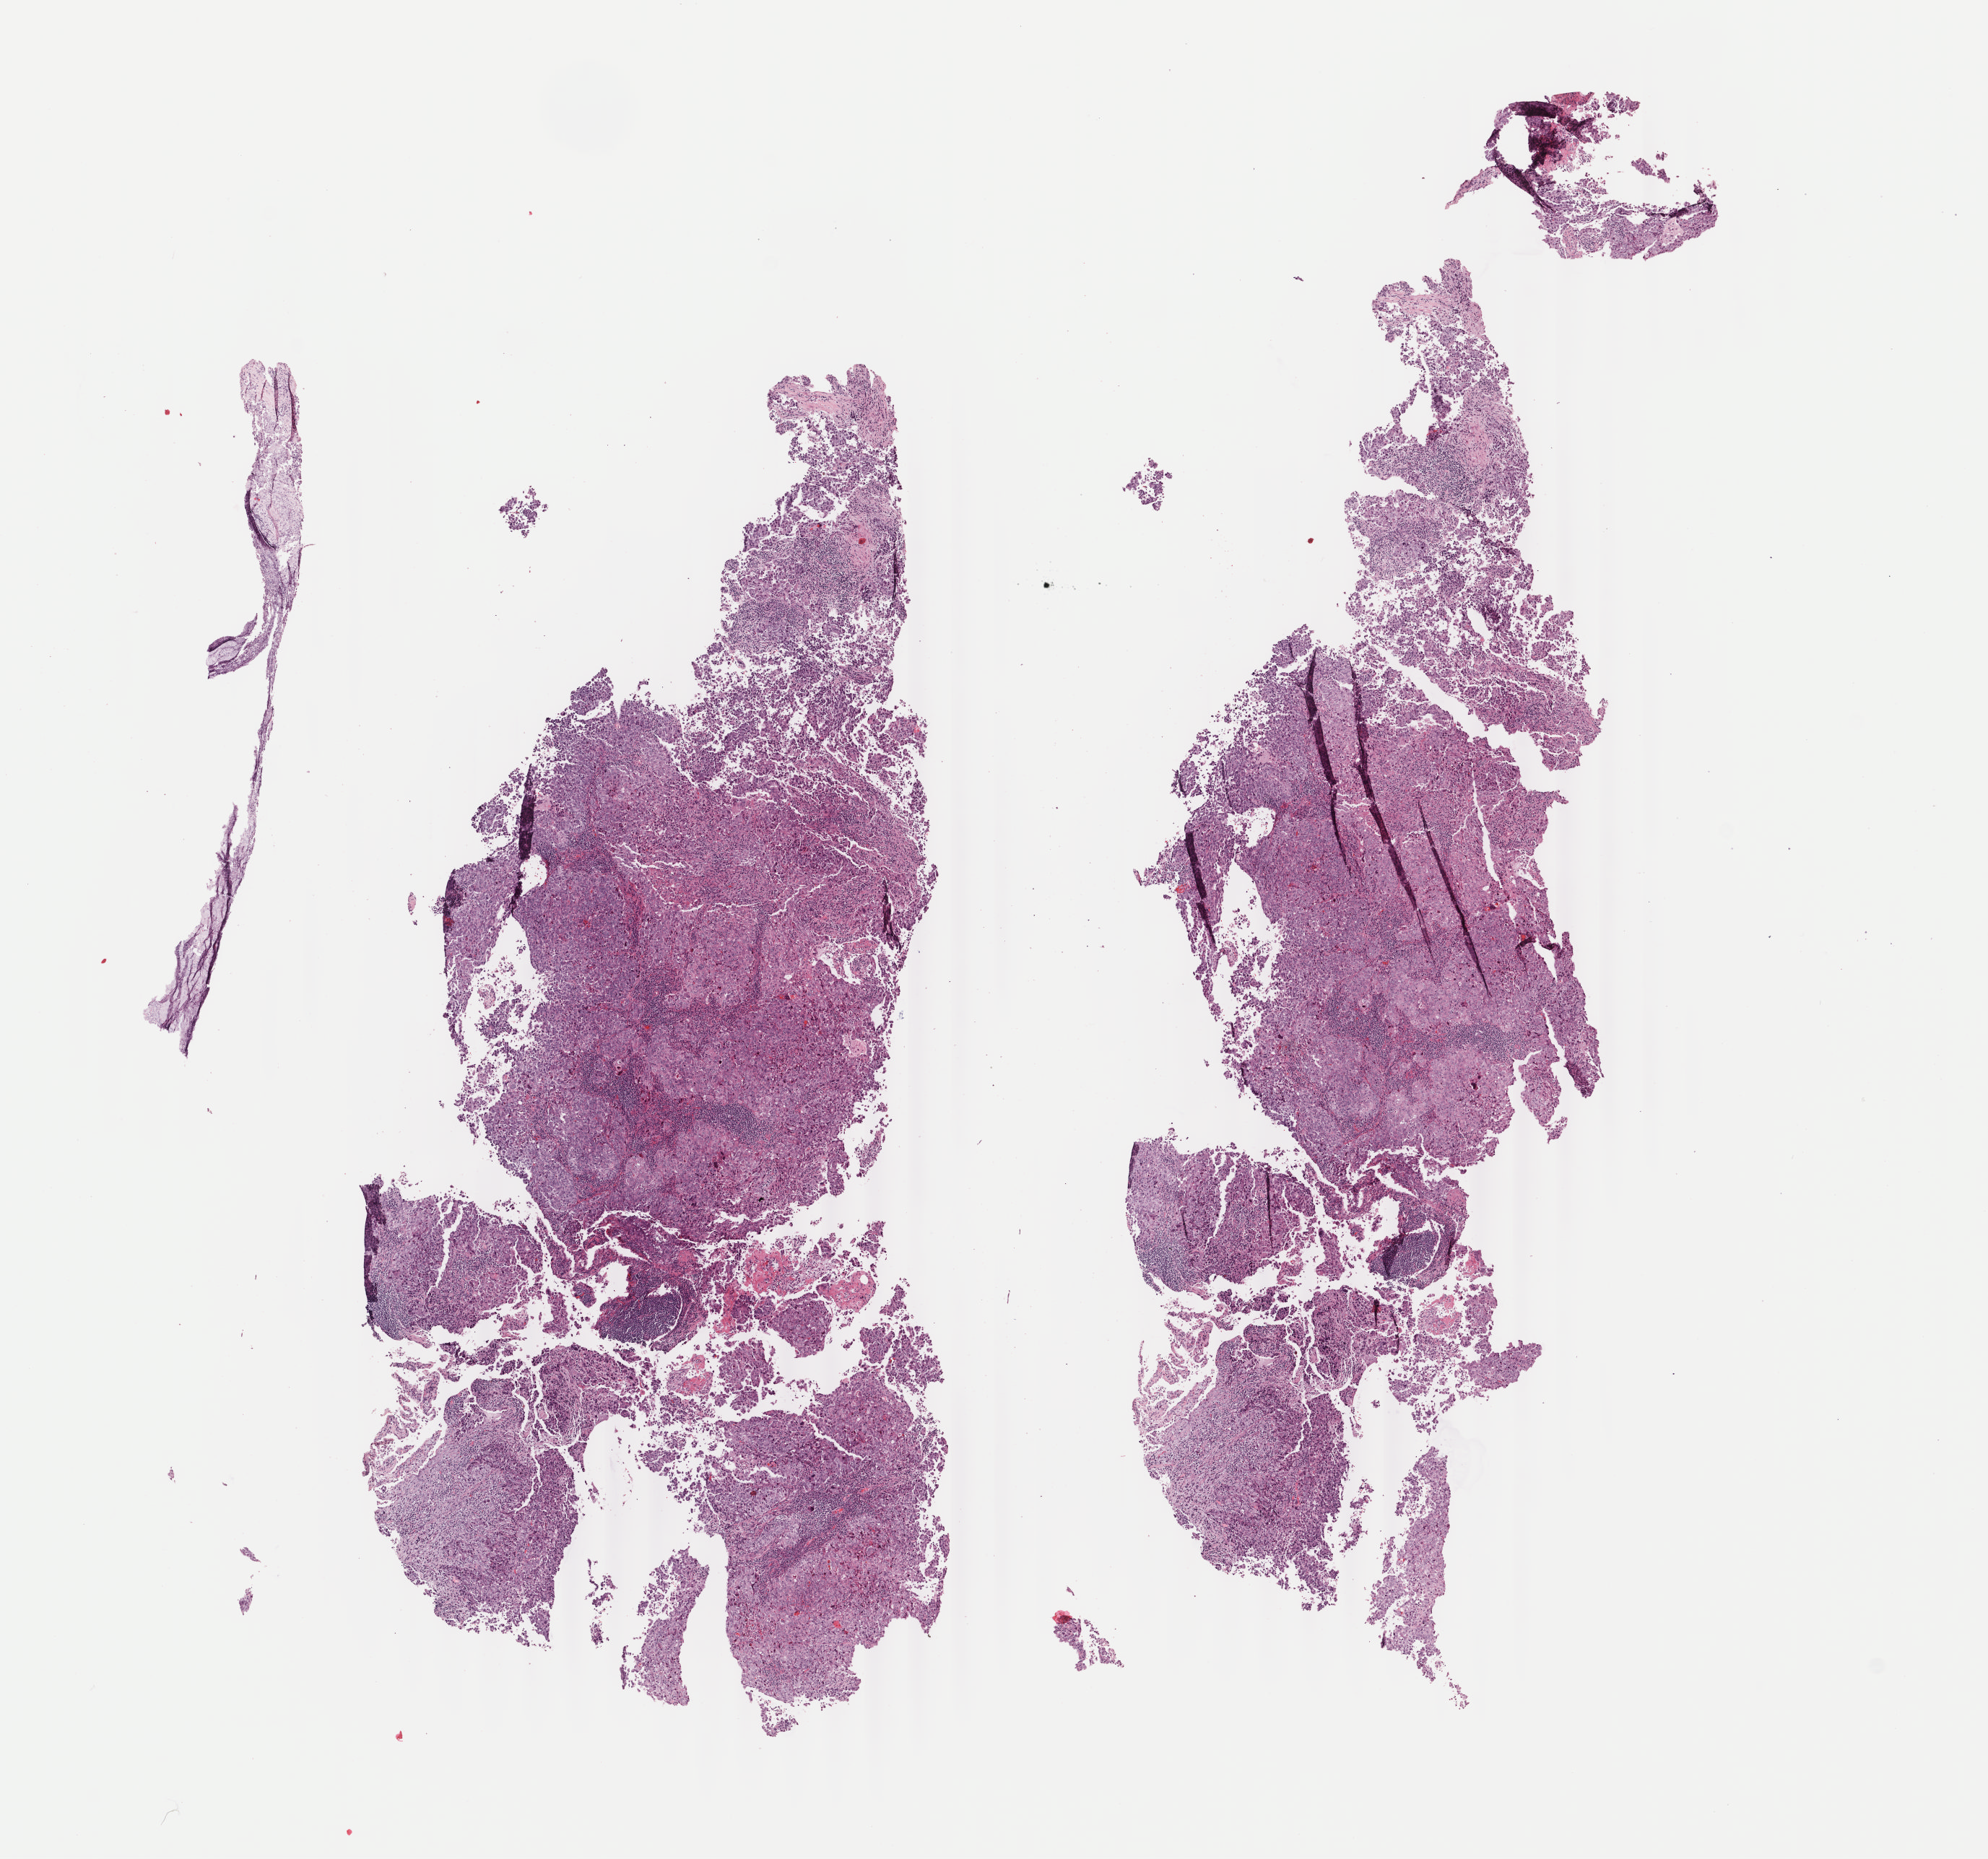
Digitized H&E-stained tissue section (whole slide) — whole scanned area (about 10.9 x 10.2 mm, acquisition: 40x scan) shown as a low-resolution overview; frozen section; sample: primary tumour, lung. Female patient; age at initial diagnosis 33 years. Pathologist review of this section (percent, as recorded): tumour cells 75%, tumour nuclei 75%, normal cells 0%, stromal cells 20%, necrosis 5%. Inflammatory infiltration, as recorded: lymphocyte infiltration 5%, monocyte infiltration 2%, neutrophil infiltration 2%.
- AJCC pathologic stage: IB (6th edition)
- diagnosis: Adenocarcinoma, NOS (upper lobe, lung)
- laterality: right